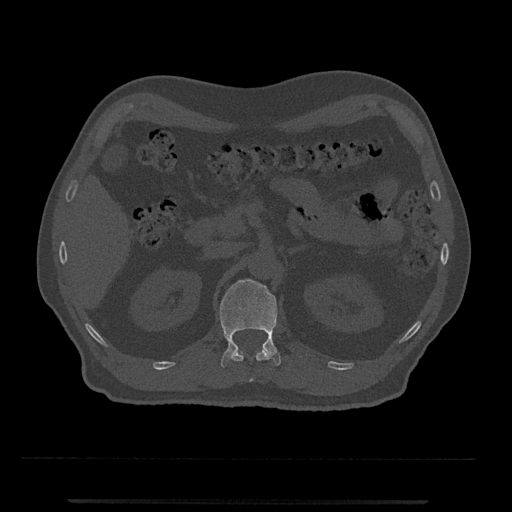
CT including the spine, one axial slice. Position 361 of 797 along the scan axis. Reconstruction kernel Br40s/3. 120 kVp. Bone window (W 1800 / L 400 HU). 0.5 mm slice thickness. 512 × 512 image matrix, field of view 419 × 419 mm. Patient: male, 63 years. From the clinical record (not read from this slice): primary cancer: prostate.
Structures marked on this image (semi-automatically segmented with operator editing):
- L1 vertebra: bounding box <220,279,281,368> (left, top, right, bottom; pixels)
- T12 vertebra: <231,348,271,382>